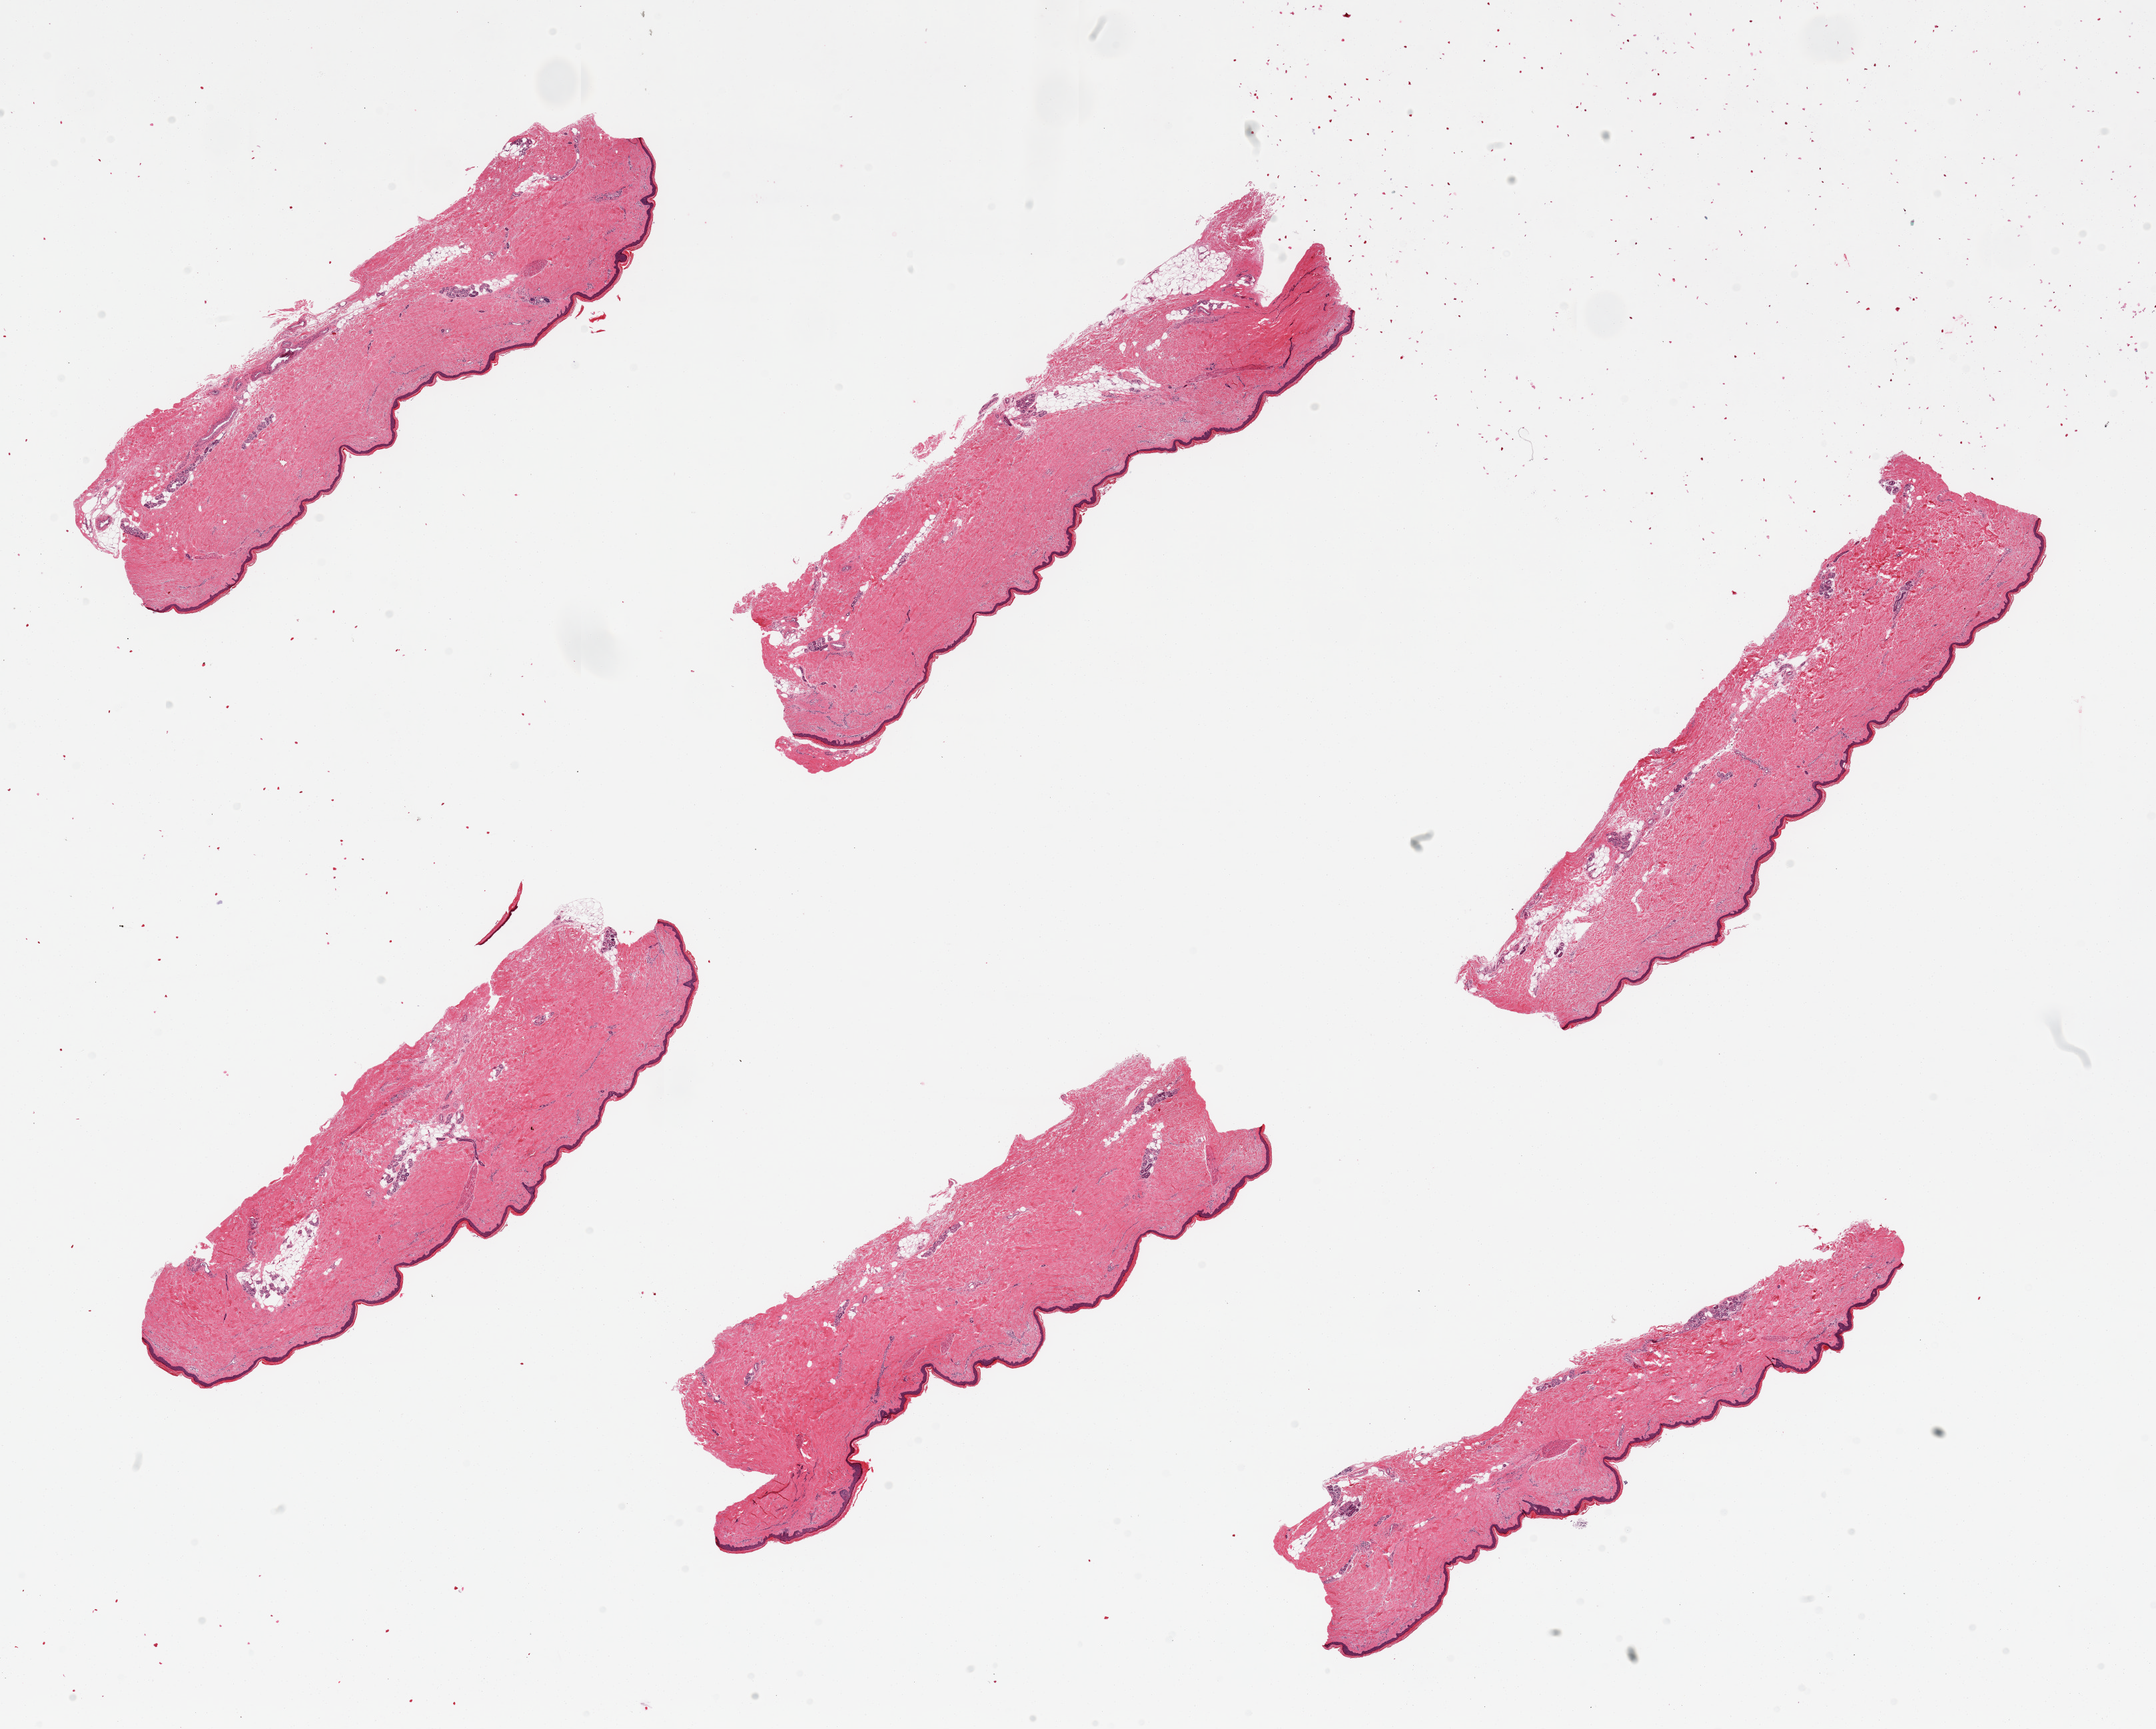
Haematoxylin and eosin whole-slide image, brightfield — shown as a low-resolution overview of the whole scanned area (about 25.6 x 20.5 mm). PAXgene-fixed, paraffin-embedded tissue. Section of skin of lower leg (target tissue). Tissue donor sample. Donor sex: female.
• pathologist's review note for this sample: 6 pieces, squamous epithelium is ~30 microns, minimal dermal fat